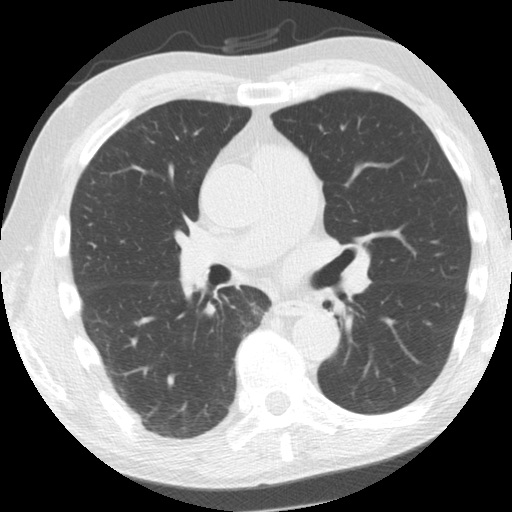
Chest CT (low-dose screening protocol), one axial image; second annual screen; lung window (W 1500 / L -600 HU); 2.5 mm slice thickness; standard (soft-tissue) reconstruction kernel (STANDARD); 512 × 512 image matrix. Male participant, aged 61 years at enrolment. Former smoker at enrolment.
Expert reader's lesion annotation, bounding box <301,289,348,327> (left, top, right, bottom; pixels). No non-calcified nodule or mass ≥4 mm was recorded by the screening reader at this exam. Participant outcome: lung cancer diagnosed 775 days after this screen (after the third annual screen) — squamous cell carcinoma, NOS, left upper lobe, left lower lobe, well differentiated (G1), stage IIB (AJCC 6th edition), 100 mm at pathology.